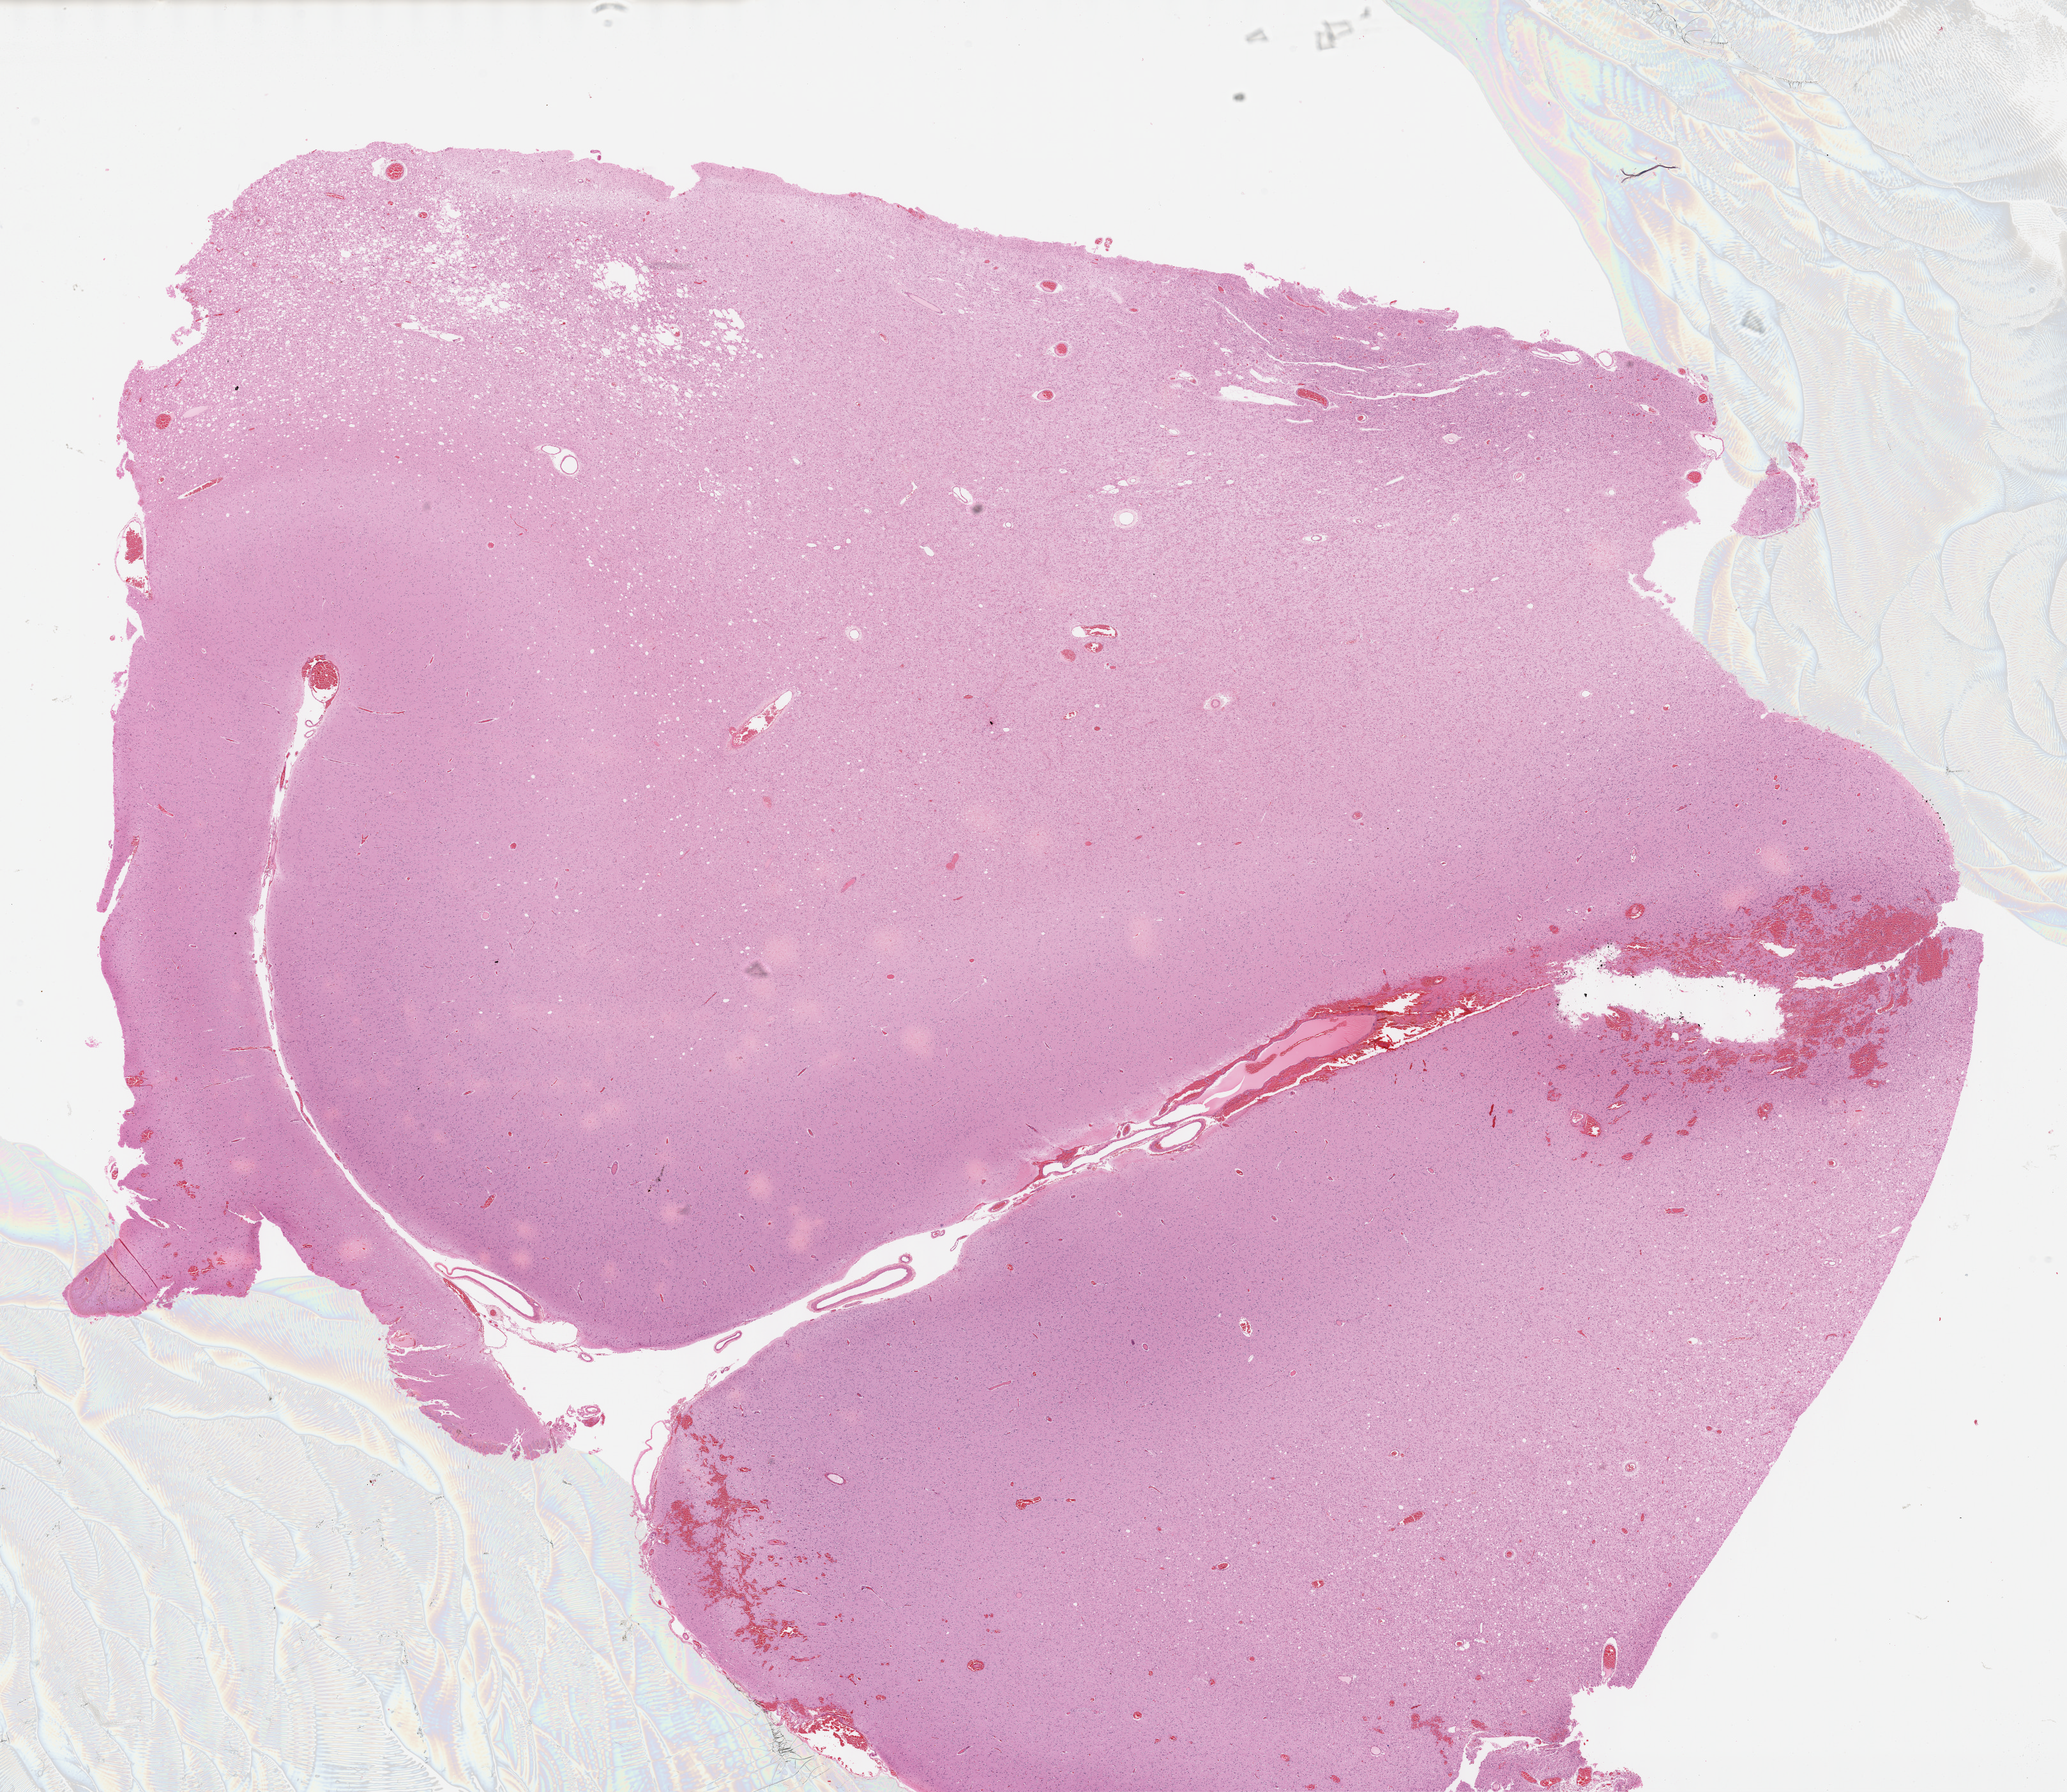
H&E-stained whole-slide image, whole scanned area (about 26.2 x 22.7 mm) shown as a low-resolution overview; formalin-fixed paraffin-embedded (FFPE) diagnostic section; primary tumour sample from the brain. Male, age 27 years at initial diagnosis. Histologic grade: G2 (moderately differentiated).
Pathologic diagnosis: Mixed glioma (cerebrum).